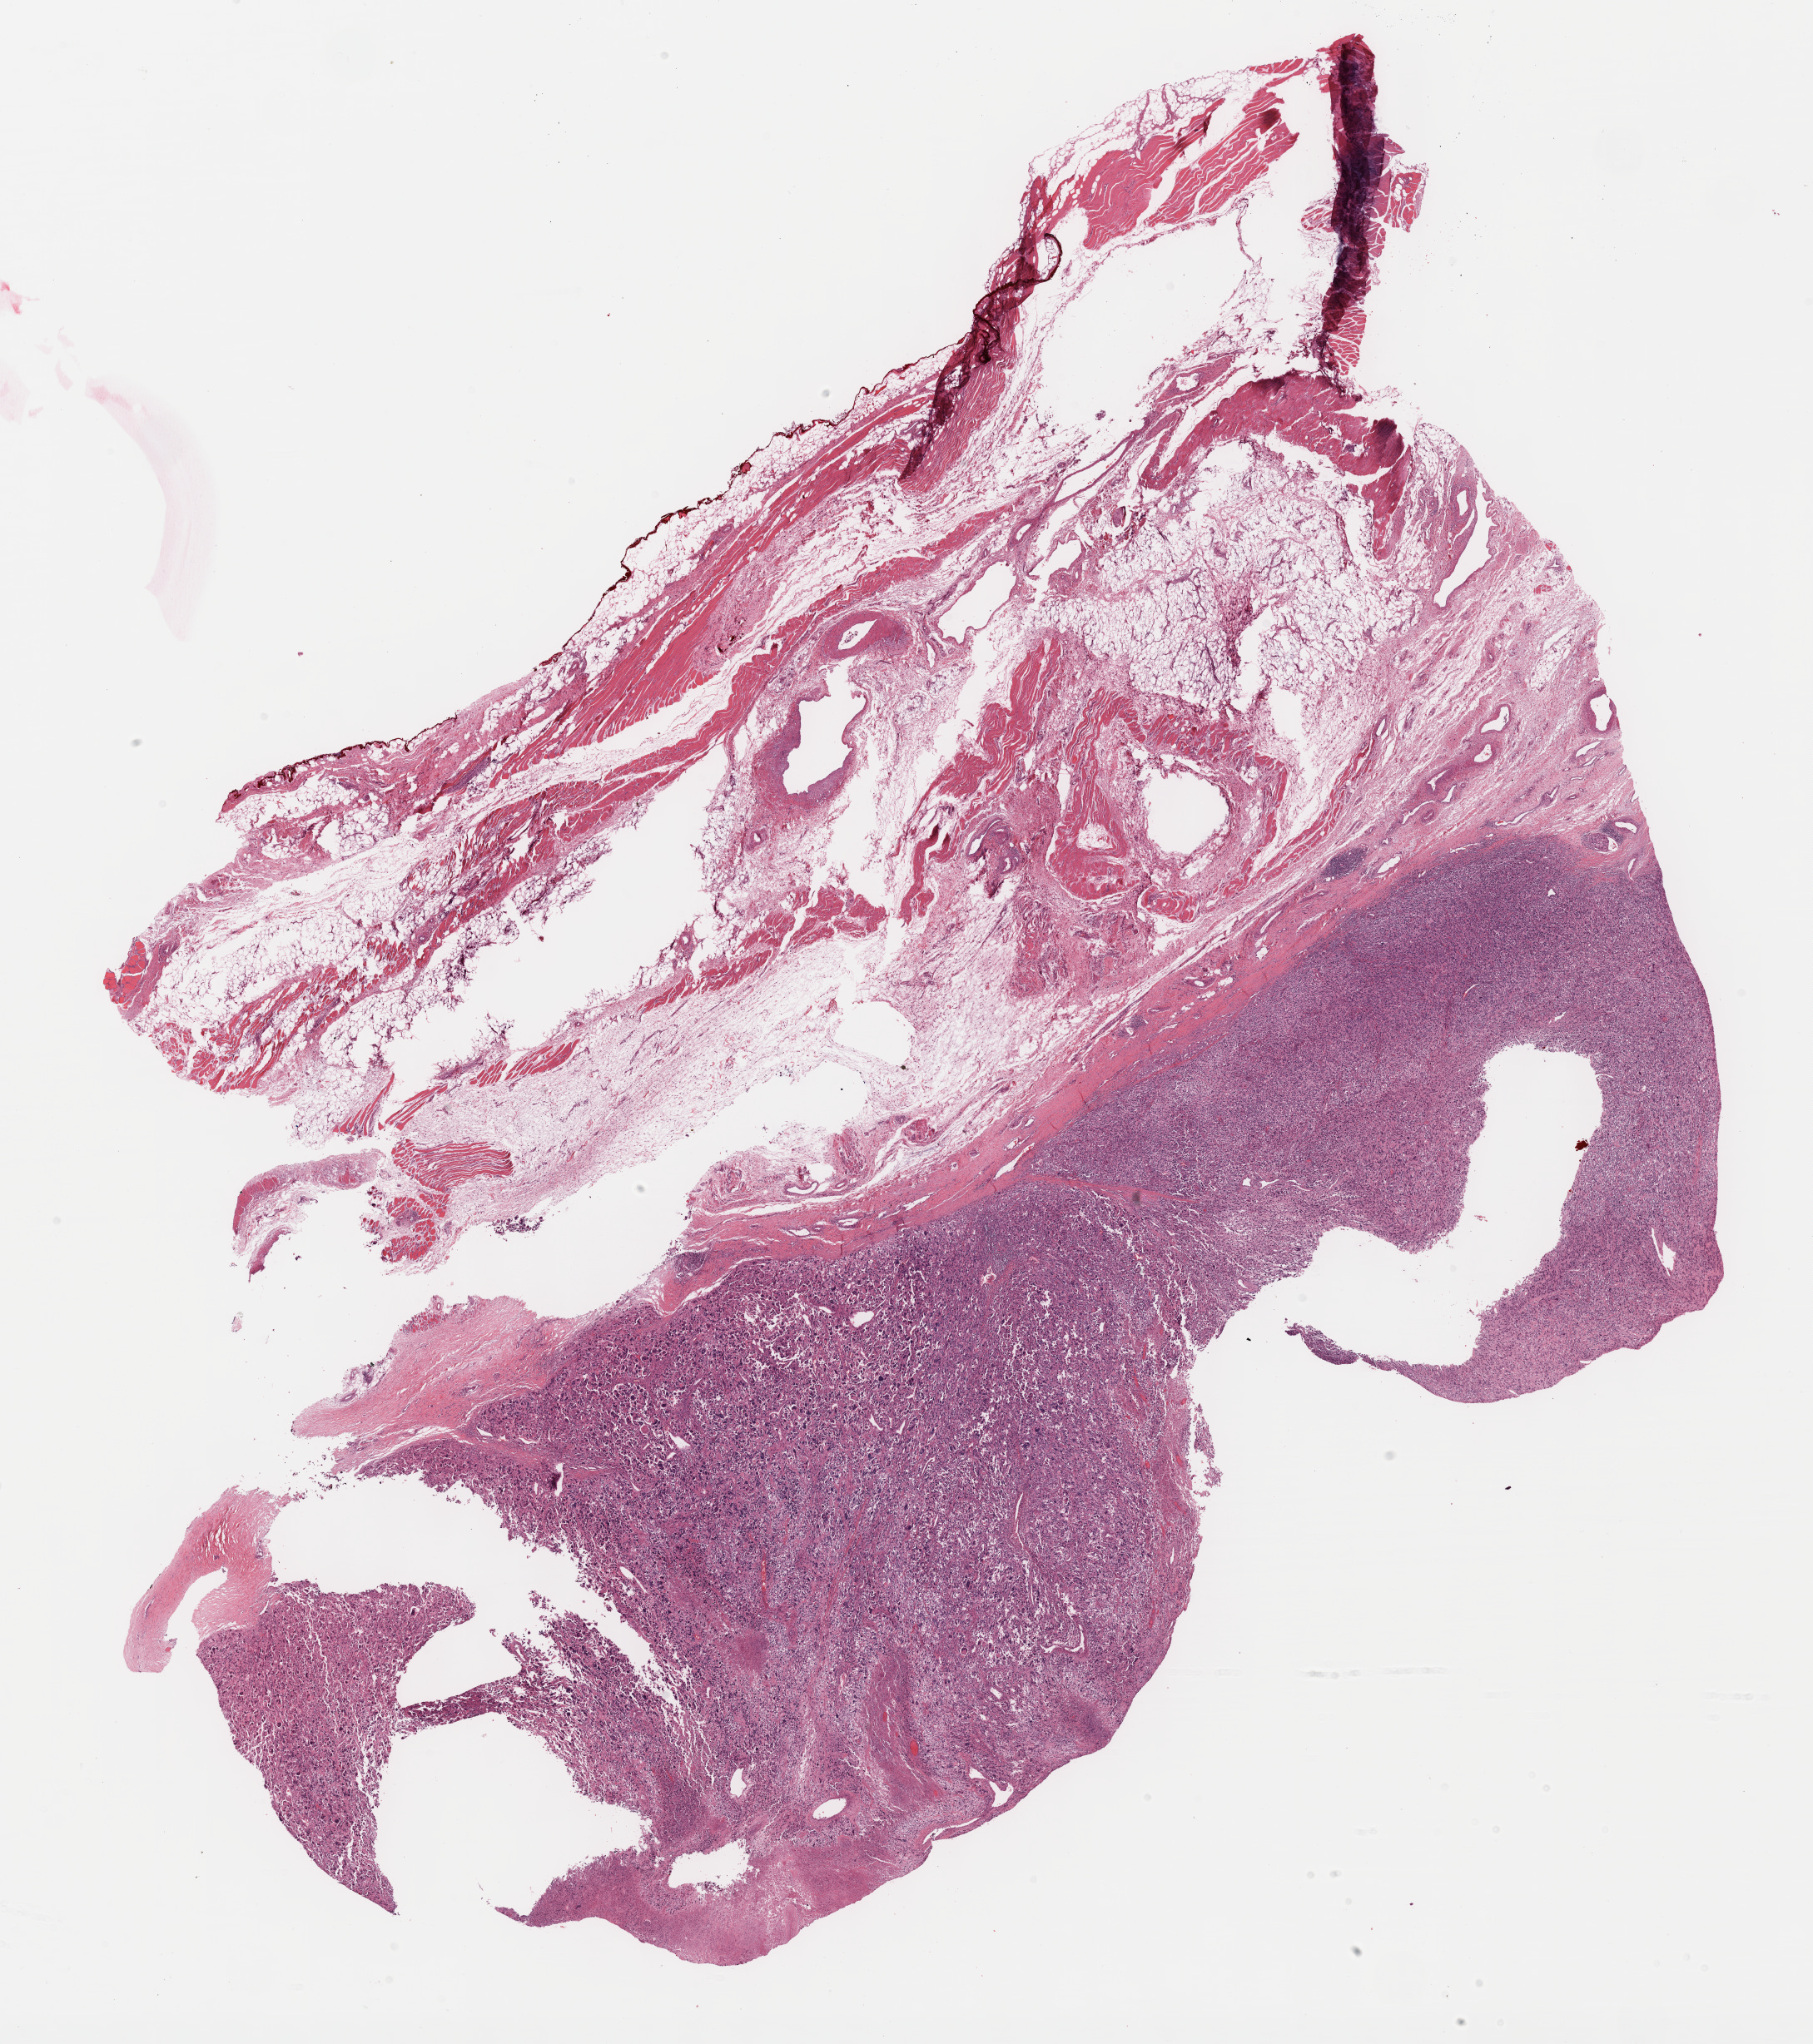
Hematoxylin and eosin (H&E) stained whole-slide image, a low-resolution overview of the entire scanned area, about 17.6 x 19.9 mm, formalin-fixed paraffin-embedded (FFPE) diagnostic section, primary tumour sample from the connective, subcutaneous and other soft tissues. Patient: male, age at initial diagnosis 58 years.
• pathologic diagnosis: Malignant fibrous histiocytoma (connective, subcutaneous and other soft tissues of lower limb and hip)